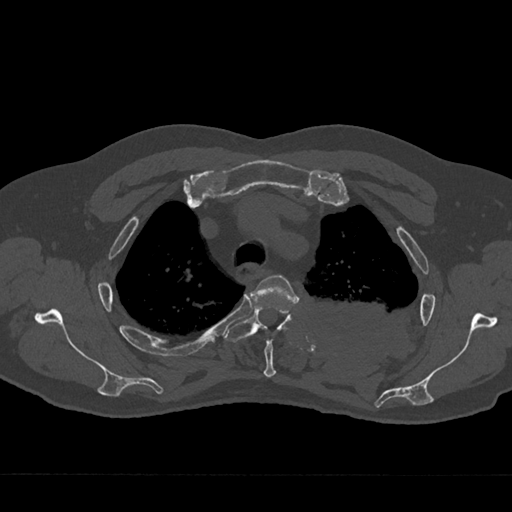
CT including the spine, one axial slice. Position 542 of 797 along the scan axis. Bone window (W 1800 / L 400 HU). 512 × 512 image matrix. Male patient, age 75 years. Case-level facts recorded for this patient, not image findings: primary cancer: renal.
Outlined on this slice (semi-automatically segmented with operator editing):
- T3 vertebra: bounding box <250,275,298,378> (left, top, right, bottom; pixels)
- T4 vertebra: <224,305,292,343>